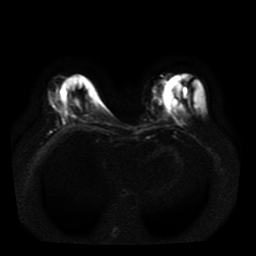
Breast MRI, one axial slice; position 12 of 41 along the scan axis; diffusion-weighted series; image 2 of 4 stored at this slice position (different b-values; order by instance number); 1.5 T; 5 mm slice thickness; 256 × 256 image matrix. Female patient.
Structures marked on this image (manually delineated by an expert):
- tumour on diffusion-weighted imaging: bounding box (x1, y1, x2, y2) in pixels: (62, 97, 68, 103)